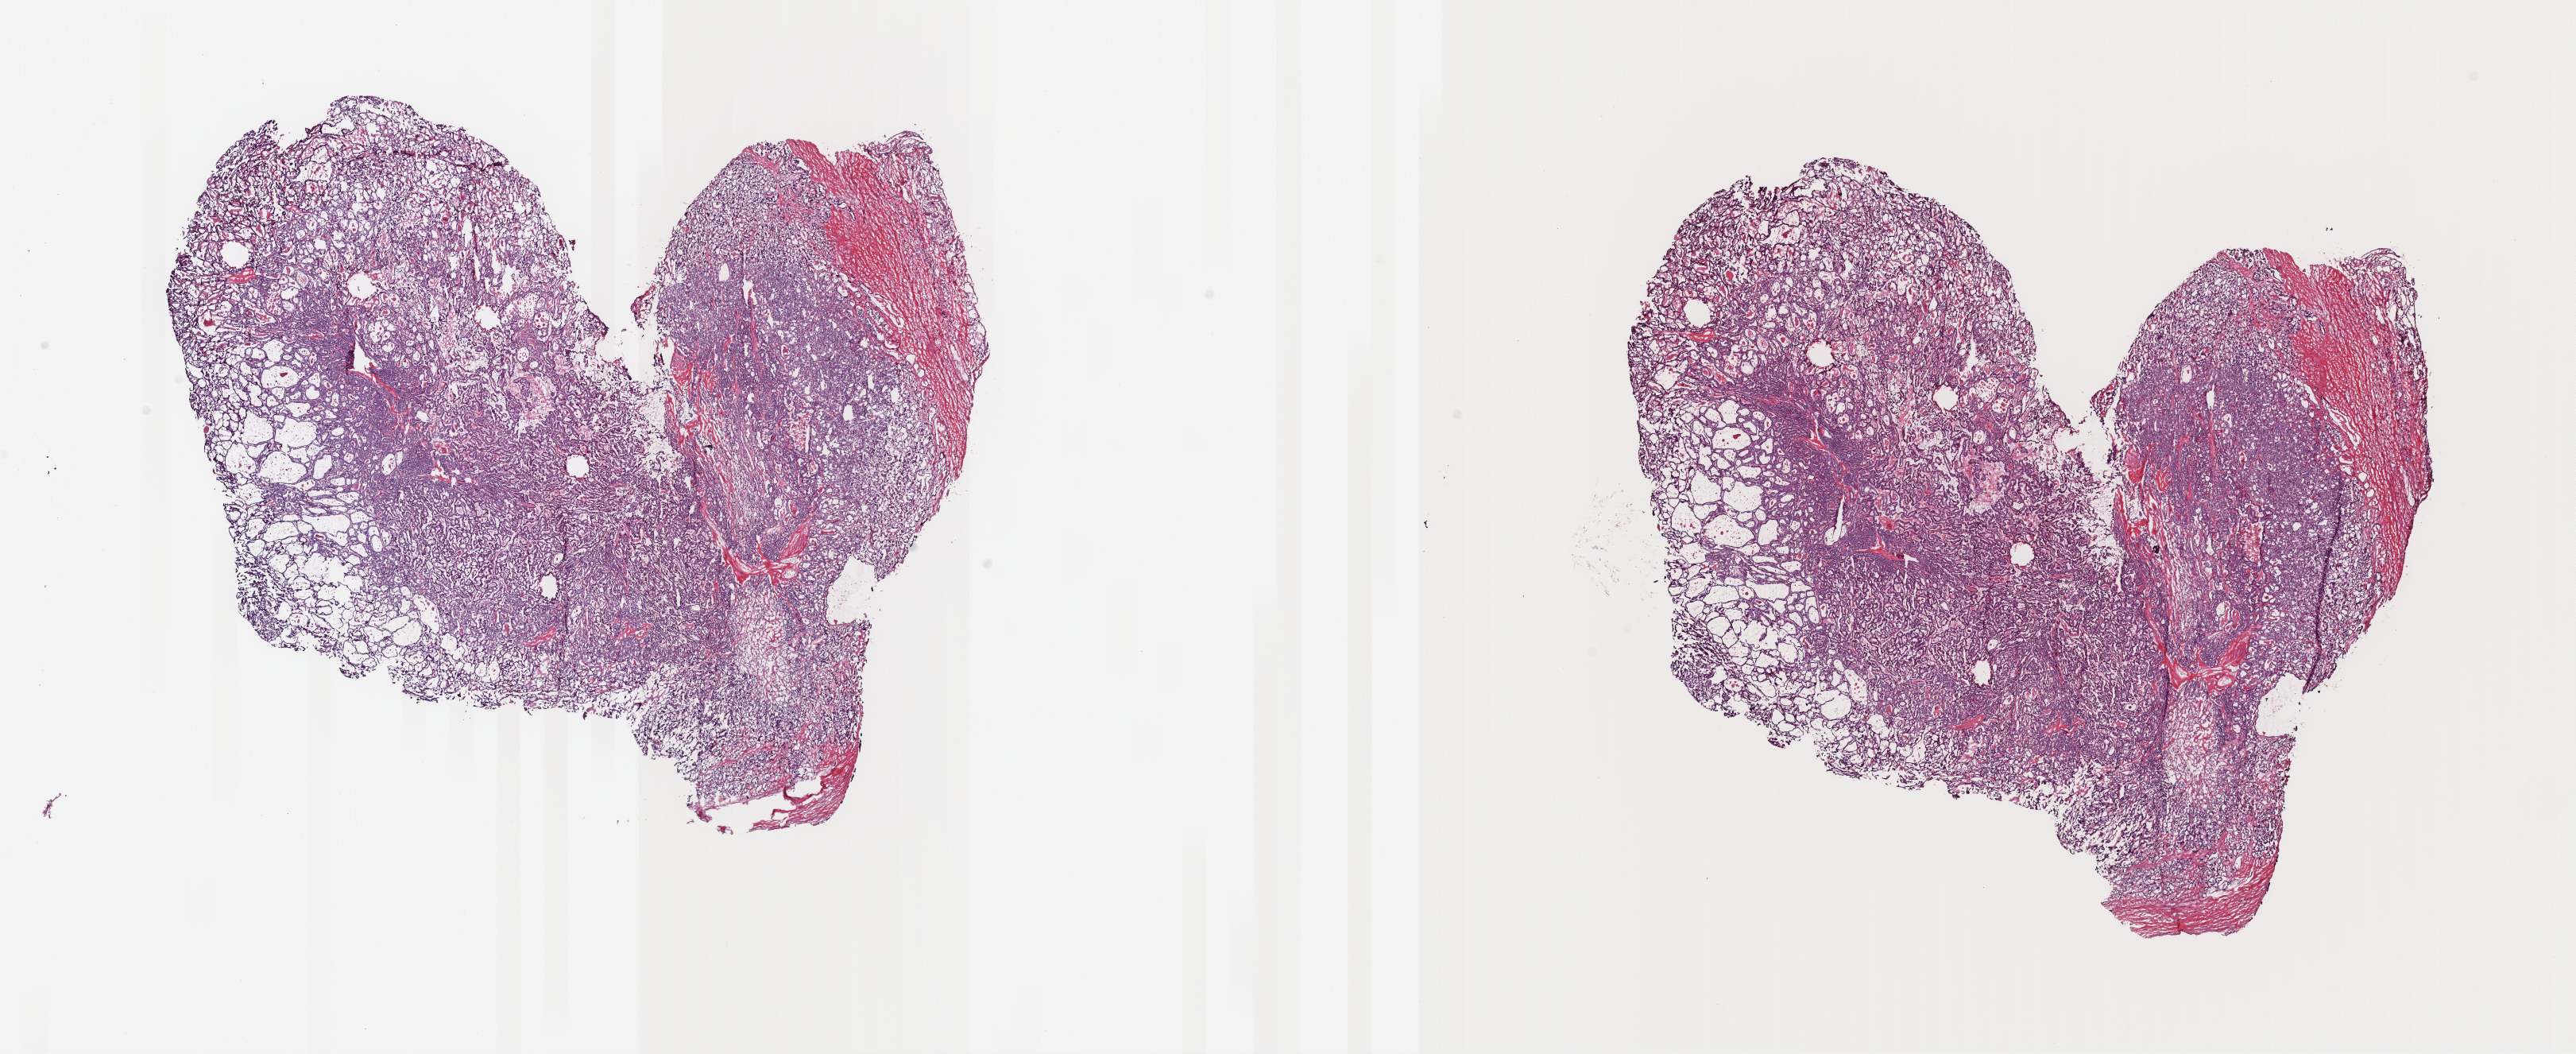
Digitized H&E-stained tissue section (whole slide), low-resolution overview of the scanned area, about 25.6 x 10.5 mm. Frozen section from the top of the tissue portion. Thyroid, primary tumour sample. Male, age 29 years at initial diagnosis. Composition of this section per pathologist review: tumour cells 92%, tumour nuclei 96%, normal cells 0%, stromal cells 8%, necrosis 0%. Infiltration values recorded for this section: lymphocyte infiltration 0%, monocyte infiltration 0%, neutrophil infiltration 0%.
- AJCC pathologic stage: I (7th edition)
- laterality: right
- pathologic diagnosis: Papillary adenocarcinoma, NOS (thyroid gland)